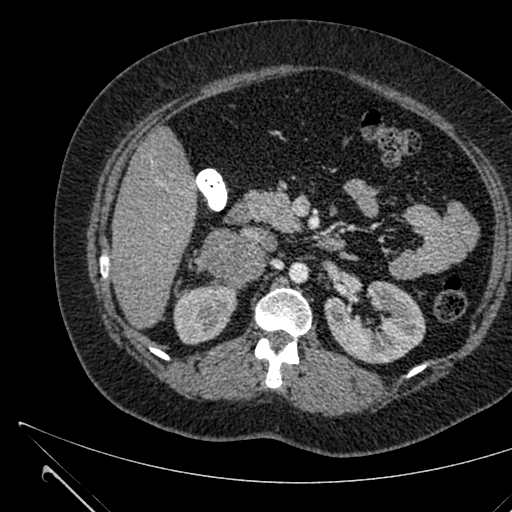
Contrast-enhanced abdominal CT, one axial slice. Position 365 of 731 along the scan axis. 120 kVp. Intravenous contrast given. Soft-tissue window (W 400 / L 40 HU). 1 mm slice thickness. 512 × 512 image matrix, field of view 376 × 376 mm. Patient: female, 36 years. Case-level facts recorded for this patient, not image findings: diagnosis: adrenocortical carcinoma; tumour side: right adrenal; tumour size at pathology: 10 cm; Ki-67 index: 20 %; stage (as recorded): 4.
Outlined on this slice (semi-automatically segmented with operator editing):
- mass: bounding box (x1, y1, x2, y2) in pixels: (201, 228, 265, 287)